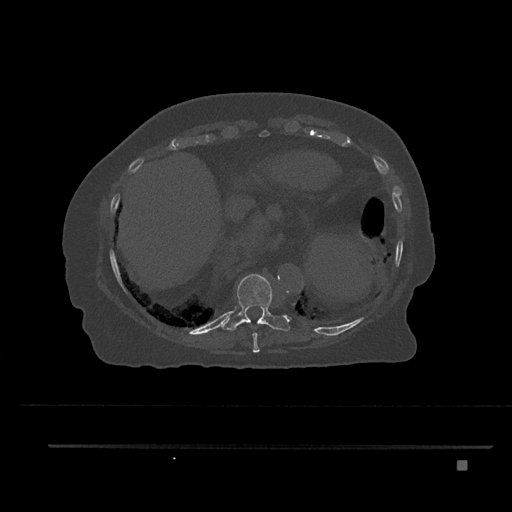
CT including the spine, one axial slice; position 365 of 797 along the scan axis; reconstruction kernel Br40s/3; 120 kVp; bone window (W 1800 / L 400 HU); 0.5 mm slice thickness; 512 × 512 image matrix. Female patient, age 76 years. From the clinical record (not read from this slice): primary cancer: lung; vertebrae with lytic lesions (as recorded): T11, L3.
Annotated regions visible in this slice (semi-automatically segmented with operator editing):
- T10 vertebra: bounding box (x1, y1, x2, y2) in pixels: (219, 274, 290, 332)
- T9 vertebra: (252, 332, 260, 353)